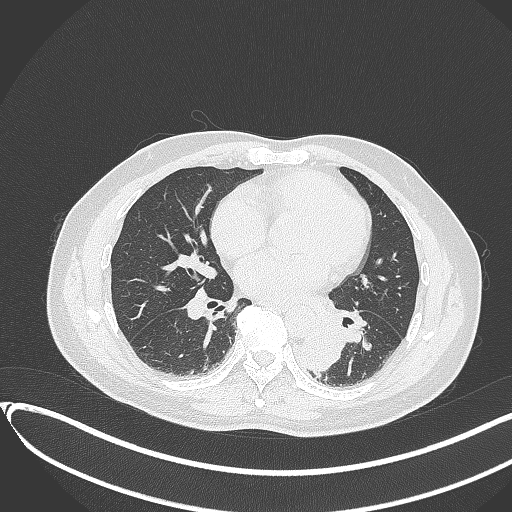
Chest CT, one axial slice; position 150 of 417 along the scan axis; reconstruction kernel B70f; lung window (W 1500 / L -600 HU); 1 mm slice thickness; 512 × 512 image matrix, field of view 400 × 400 mm. Male patient, age 54 years. From the clinical record (not read from this slice): clinical TNM (as recorded): T3 N0 M0.
Structures marked on this image (bounding box drawn by a radiologist):
- lung tumour (recorded histology: squamous cell carcinoma): bounding box (x1, y1, x2, y2) in pixels: (296, 325, 344, 374)